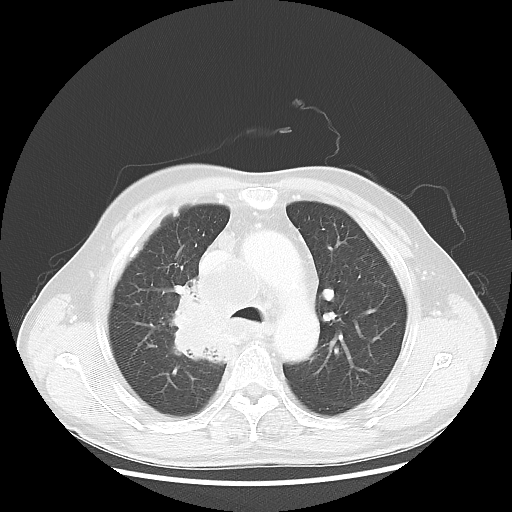
Chest CT, one axial slice. Slice 40 of 60 in the series (ordered by position). Reconstruction kernel LUNG. 100 kVp. Lung window (W 1500 / L -600 HU). 5 mm slice thickness. 512 × 512 image matrix, field of view 382 × 382 mm. Male patient, age 64 years. From the clinical record (not read from this slice): clinical TNM (as recorded): T3 N3 M0; histopathological grade: G3.
Structures marked on this image (bounding box drawn by a radiologist):
- lung tumour (recorded histology: small cell carcinoma): bounding box (x1, y1, x2, y2) in pixels: (160, 283, 242, 370)